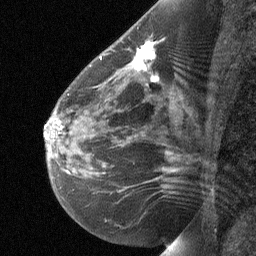
Breast MRI (dynamic contrast-enhanced), one sagittal slice; slice 36 of 64 in the series (ordered by position); dynamic contrast-enhanced study with each time point stored as its own series, time point 2 of 3 at this slice position (early post-contrast, ordered by acquisition time); 1.5 T; TE 4.8 ms, TR 27 ms; 2 mm slice thickness; 256 × 256 image matrix, field of view 180 × 180 mm. Patient: female, 51 years. From the clinical record (not read from this slice): setting: breast cancer imaged before/during neoadjuvant chemotherapy; receptor status: HR-positive, HER2-negative.
Outlined on this slice (semi-automatically segmented with operator editing):
- analysis volume of interest (the breast-tissue region the enhancement analysis was run in; not a lesion): bounding box (x1, y1, x2, y2) in pixels: (81, 35, 179, 103)
- tumour enhancement mask (voxels above the 90 % enhancement threshold inside the analysis volume of interest): (133, 43, 155, 79)